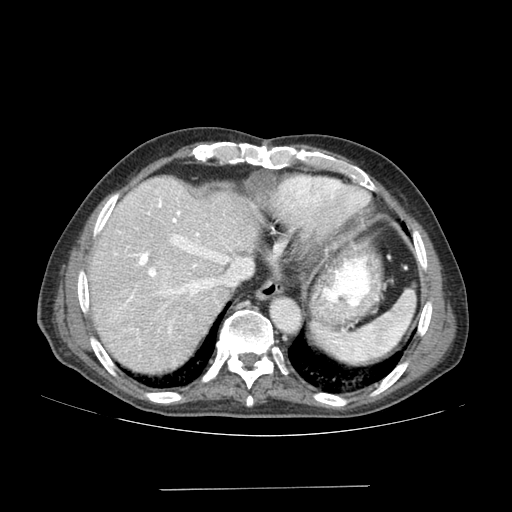
Contrast-enhanced abdominal CT (liver protocol), one axial slice; position 140 of 192 along the scan axis; 120 kVp; soft-tissue window (W 400 / L 40 HU); 512 × 512 image matrix, field of view 400 × 400 mm. From the clinical record (not read from this slice): diagnosis: hepatocellular carcinoma (patient treated with transarterial chemoembolisation; whether this scan precedes or follows treatment is not stated here); TNM stage (as recorded): Stage-IVA; Child-Pugh class: A; tumour differentiation: poorly differentiated.
Outlined on this slice (semi-automatically segmented with operator editing):
- abdominal aorta: bounding box <272,299,299,330> (left, top, right, bottom; pixels)
- liver parenchyma outside the tumour (the mass and vessels are separate outlines, so this box may not span the whole liver): <88,176,260,374>
- mass: <142,264,182,294>
- liver vessels: <127,199,229,333>